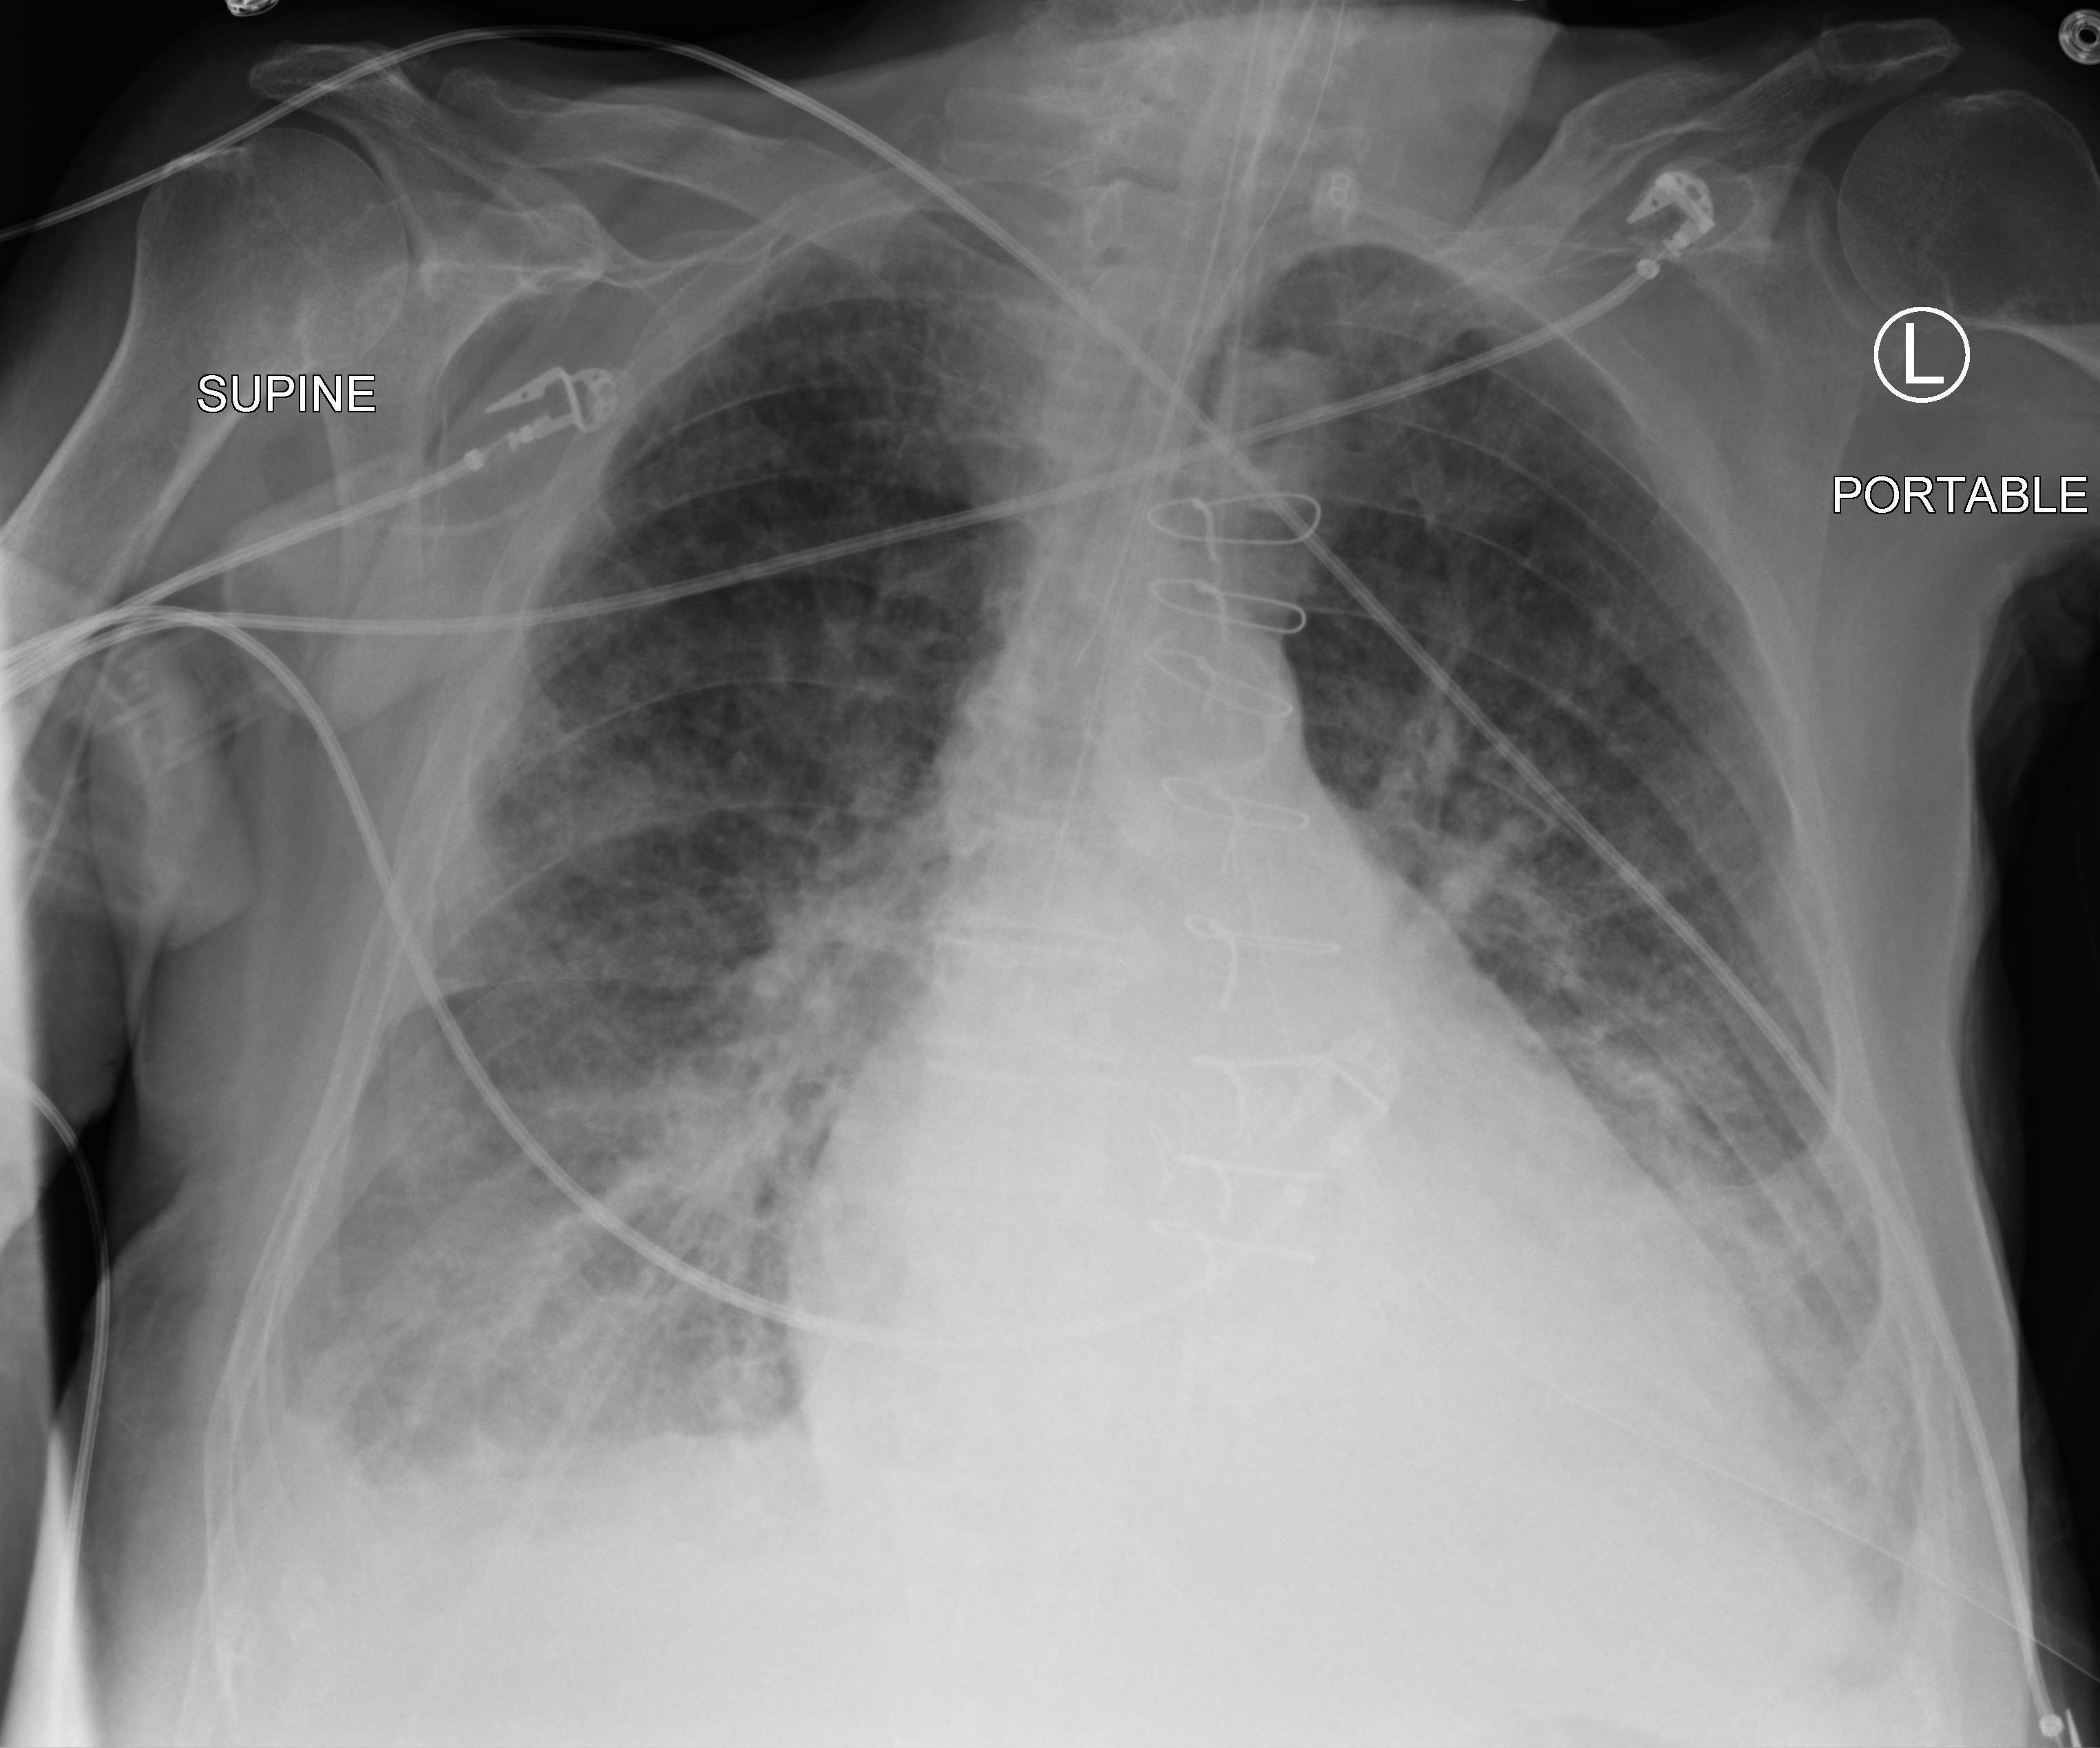
Chest X-ray (portable); anteroposterior (AP) projection. Patient hospitalised with COVID-19; male, aged 75–90 years.
Admission-level facts for this patient (not findings on this image; timing relative to this image not recorded): admitted to intensive care during this hospital stay: yes.